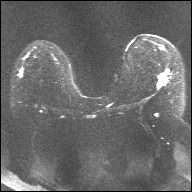
Breast MRI, one axial slice. Slice 17 of 32 in the series (ordered by position). Diffusion-weighted series; image 2 of 4 stored at this slice position (different b-values; order by instance number). 1.5 T. 4 mm slice thickness. 192 × 192 image matrix, field of view 360 × 360 mm. Female patient.
Outlined on this slice (manually delineated by an expert):
- tumour on diffusion-weighted imaging: bounding box (x1, y1, x2, y2) in pixels: (159, 75, 165, 86)